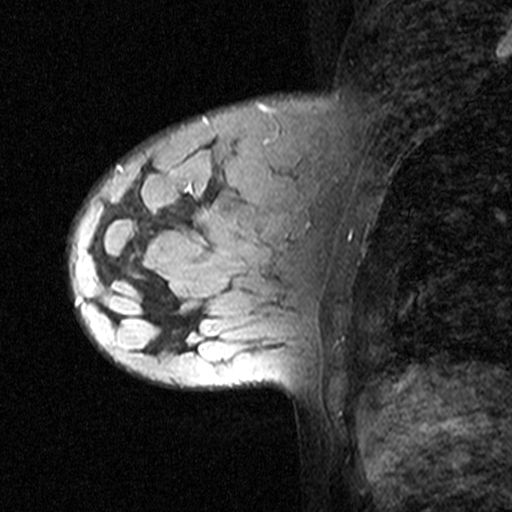
Breast MRI (dynamic contrast-enhanced), one sagittal slice. Slice 13 of 44 in the series (ordered by position). Dynamic contrast-enhanced study with each time point stored as its own series, time point 2 of 3 at this slice position (early post-contrast, ordered by acquisition time). 1.5 T. TE 4.5 ms, TR 11 ms. 3 mm slice thickness. 512 × 512 image matrix, field of view 200 × 200 mm. Female patient, age 27 years. From the clinical record (not read from this slice): setting: breast cancer imaged before/during neoadjuvant chemotherapy; receptor status: HR-positive, HER2-negative.
Structures marked on this image (semi-automatically segmented with operator editing):
- analysis volume of interest (the breast-tissue region the enhancement analysis was run in; not a lesion): box from (x=68, y=162) to (x=163, y=271) px
- tumour enhancement mask (voxels above the 90 % enhancement threshold inside the analysis volume of interest): (x=117, y=165)–(x=124, y=171)